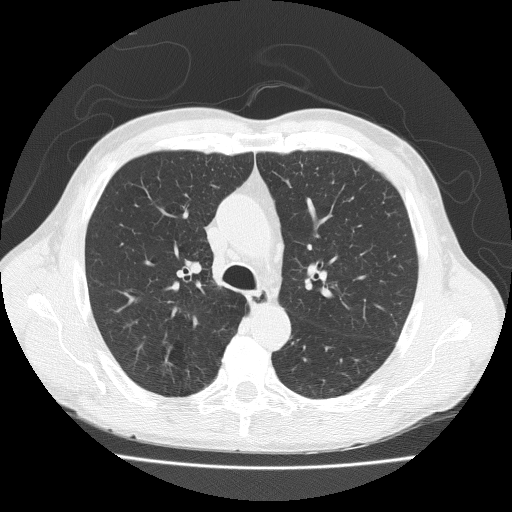
Low-dose screening chest CT, axial slice; first (baseline) screen; lung window (W 1500 / L -600 HU); slice 67 of 203 in the series. Male participant, aged 73 years at enrolment.
• Expert reader's lesion annotation, box from (x=145, y=340) to (x=198, y=388) px.
• No non-calcified nodule or mass ≥4 mm was recorded by the screening reader at this exam.